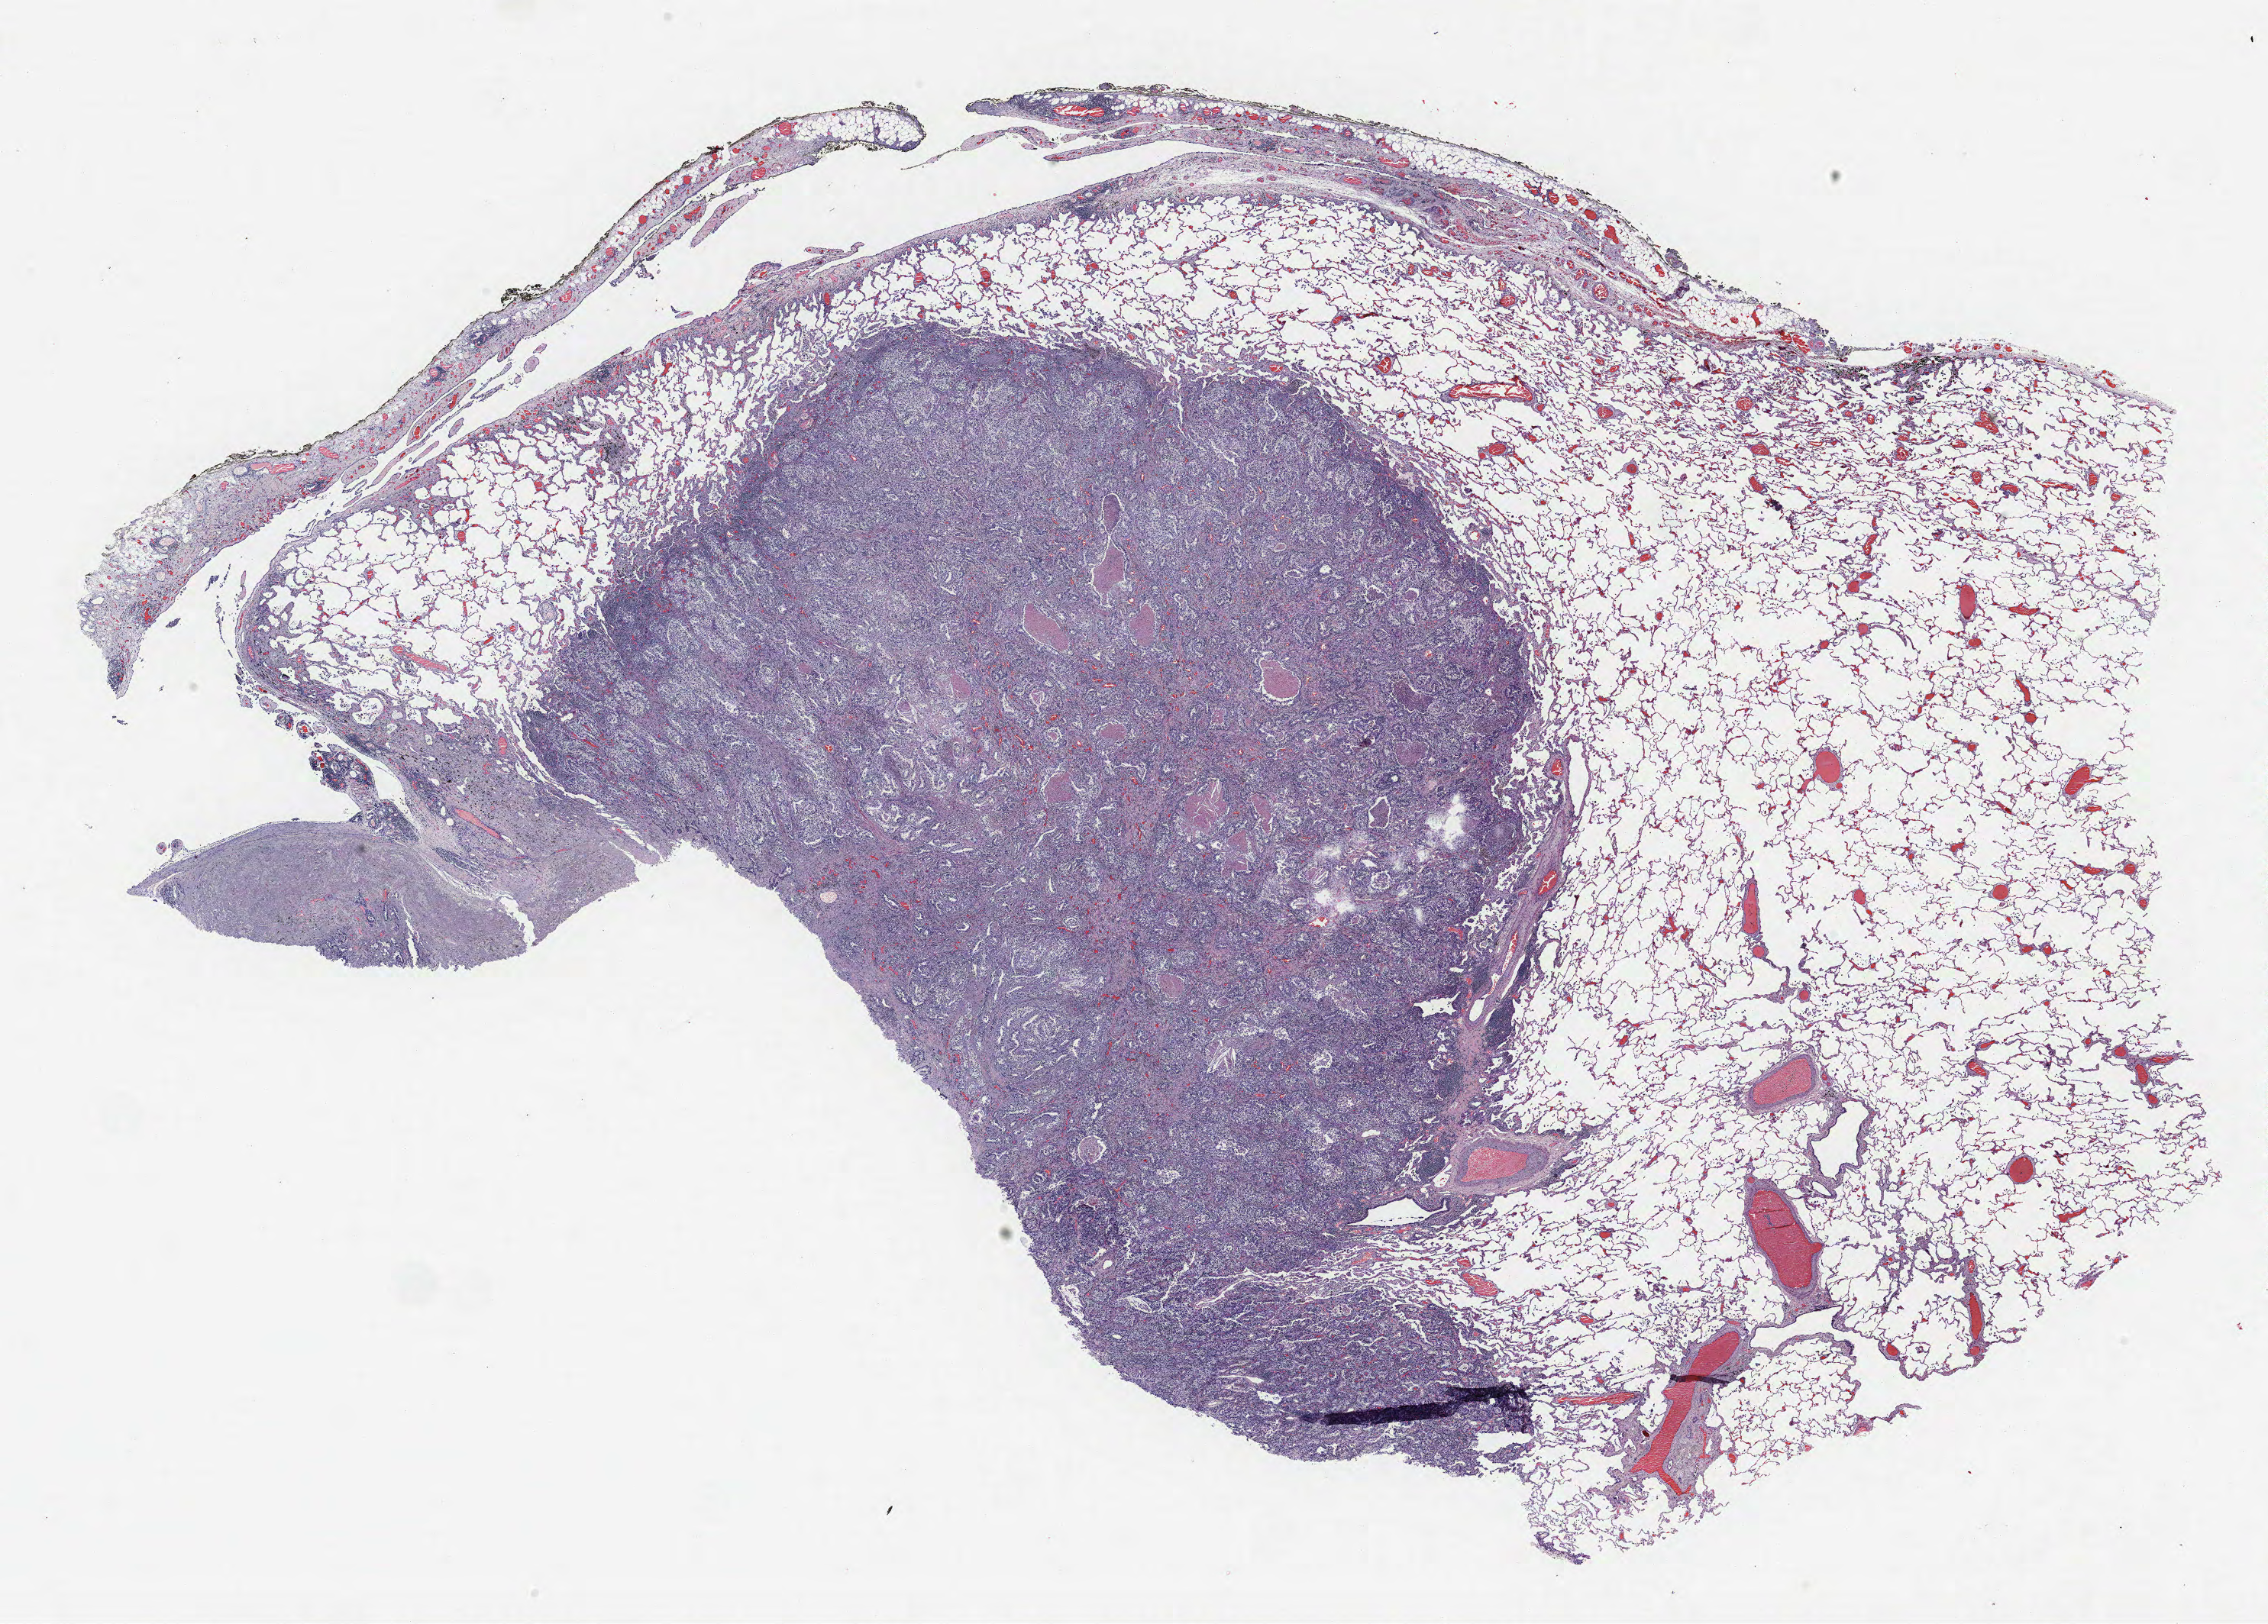
Whole-slide histology image, H&E-stained, whole scanned area (about 23.8 x 17.0 mm, acquisition: 40x scan) shown as a low-resolution overview; formalin-fixed paraffin-embedded (FFPE) section; lung tissue. Male, age 68 at enrolment. Current smoker at enrolment. Grade: well differentiated (G1).
* participant's lung-cancer diagnosis: Adenocarcinoma, NOS (ICD-O-3 8140/3)
* primary tumour location (clinical record): right upper lobe, right lower lobe
* stage (AJCC 6th edition): IV
* tumour size (pathology): 35 mm